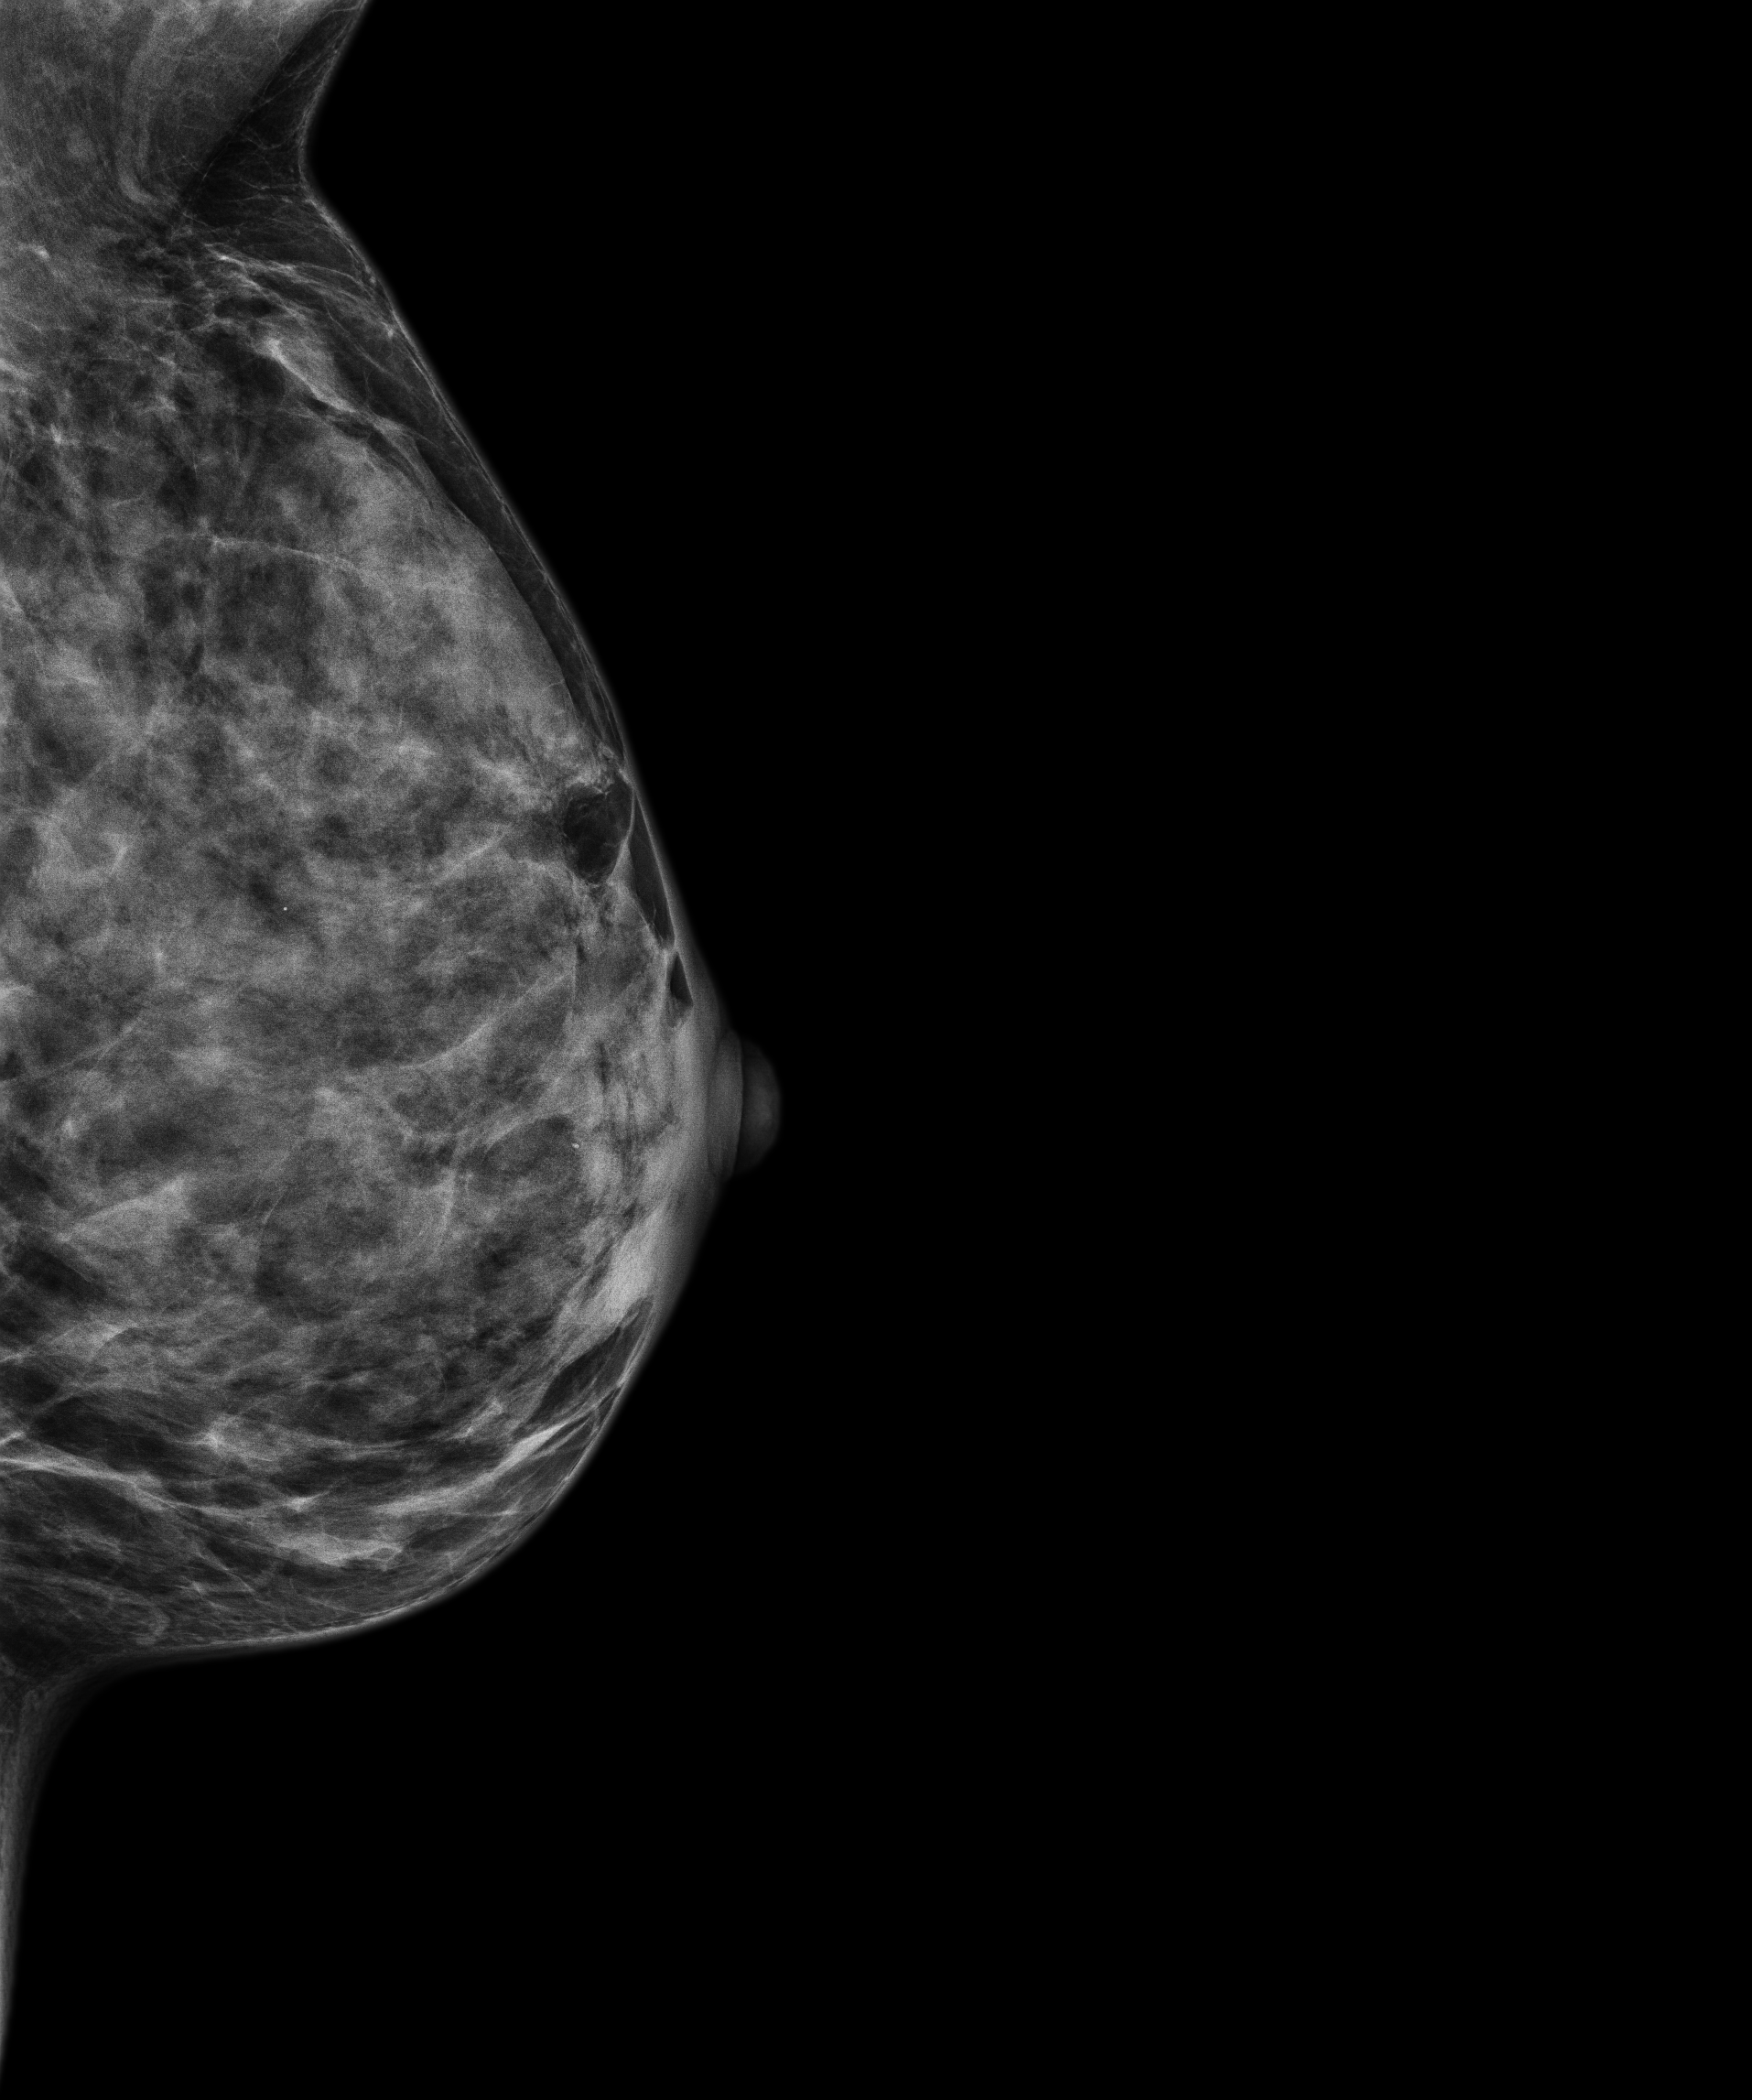
Screening examination. Patient: female, 46 years.
Image type: full-field digital mammogram. Breast: left. Projection: mediolateral oblique (MLO) view.